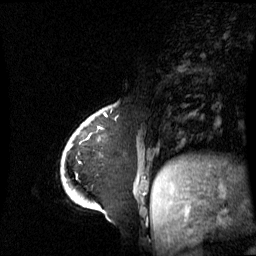
Breast MRI (dynamic contrast-enhanced), one sagittal slice. Slice 16 of 60 in the series (ordered by position). Dynamic contrast-enhanced series, image 2 of 3 at this slice position (ordered by acquisition). 1.5 T. TE 4.2 ms, TR 8.4 ms. 2.8 mm slice thickness. 256 × 256 image matrix. Patient: female, 43 years. From the clinical record (not read from this slice): setting: breast cancer imaged before/during neoadjuvant chemotherapy; receptor status: triple-negative.
Structures marked on this image (semi-automatic segmentation, software-assisted and operator-edited):
- analysis volume of interest (the breast-tissue region the enhancement analysis was run in; not a lesion): bounding box (x1, y1, x2, y2) in pixels: (65, 118, 143, 198)
- tumour enhancement mask (voxels above the 70 % enhancement threshold inside the analysis volume of interest): (67, 148, 69, 150)